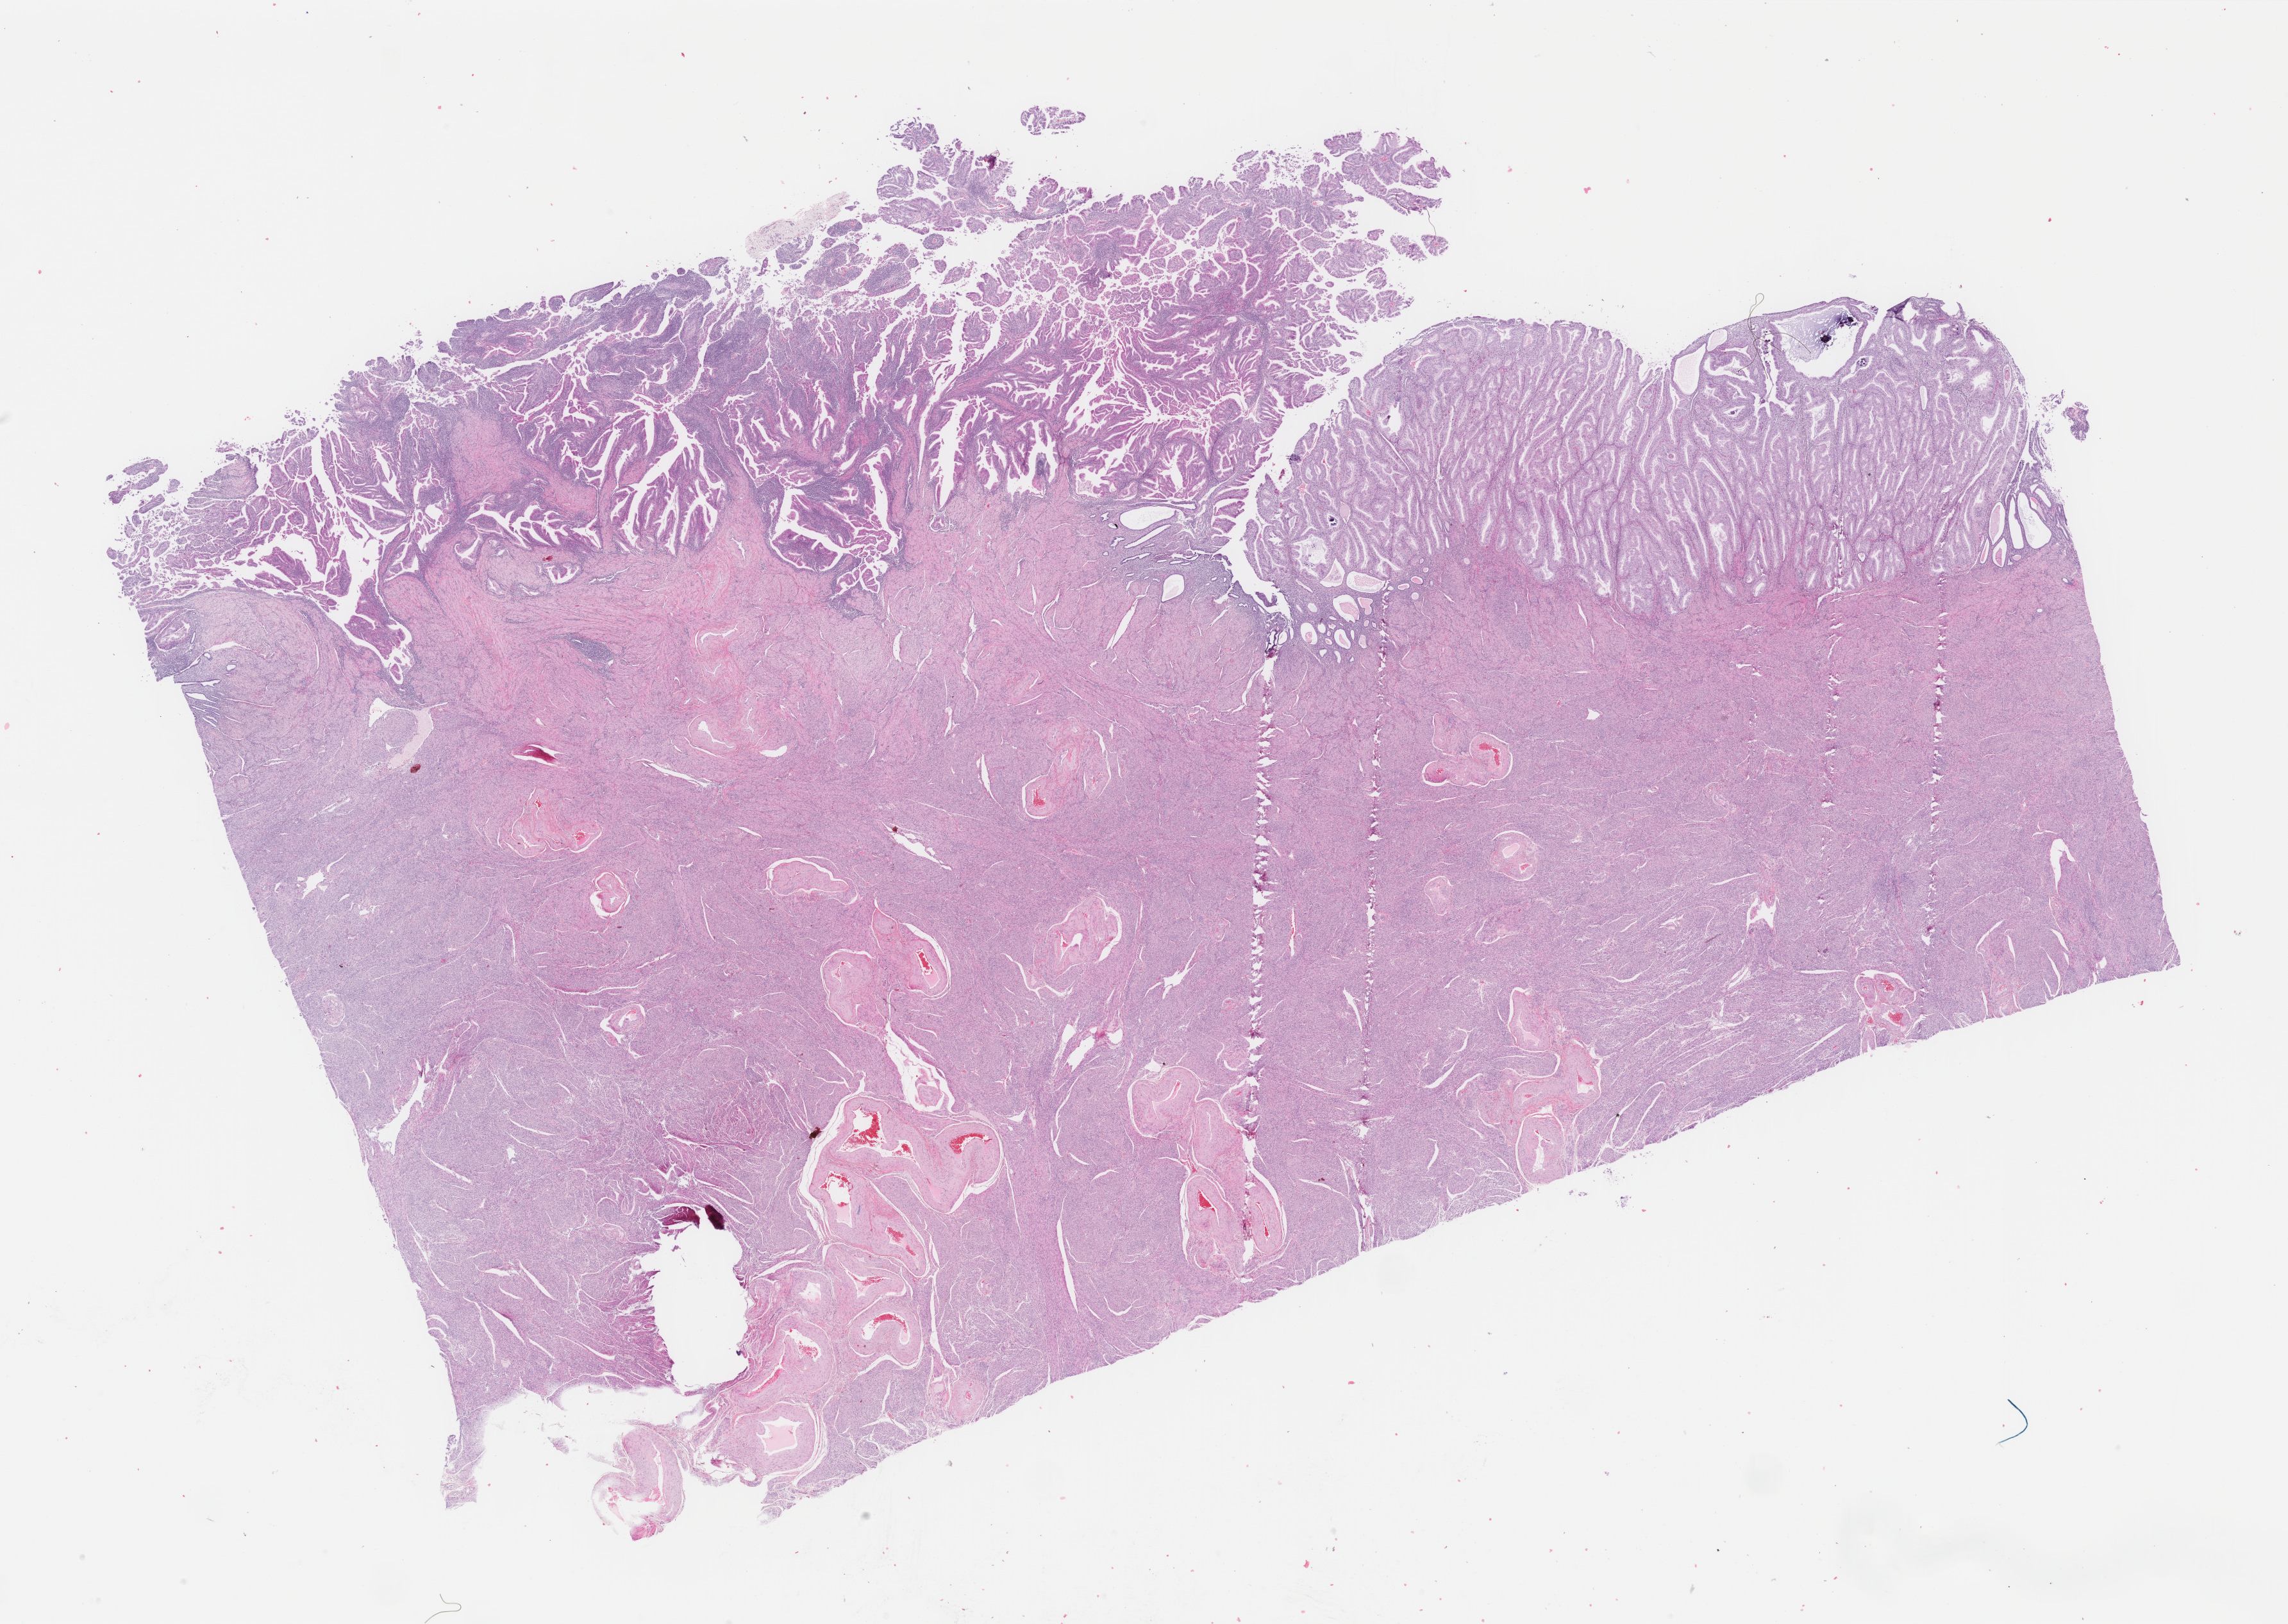
Whole-slide histology image, Hematoxylin and eosin (H&E) stained, whole scanned area (about 28.3 x 20.1 mm, acquisition: 40x scan) shown as a low-resolution overview, formalin-fixed paraffin-embedded (FFPE) diagnostic section, primary tumour sample from the uterus. Female patient; age at initial diagnosis 69 years. Histologic grade: G1 (well differentiated).
FIGO stage: IA. Pathologic diagnosis: Endometrioid adenocarcinoma, NOS (endometrium).